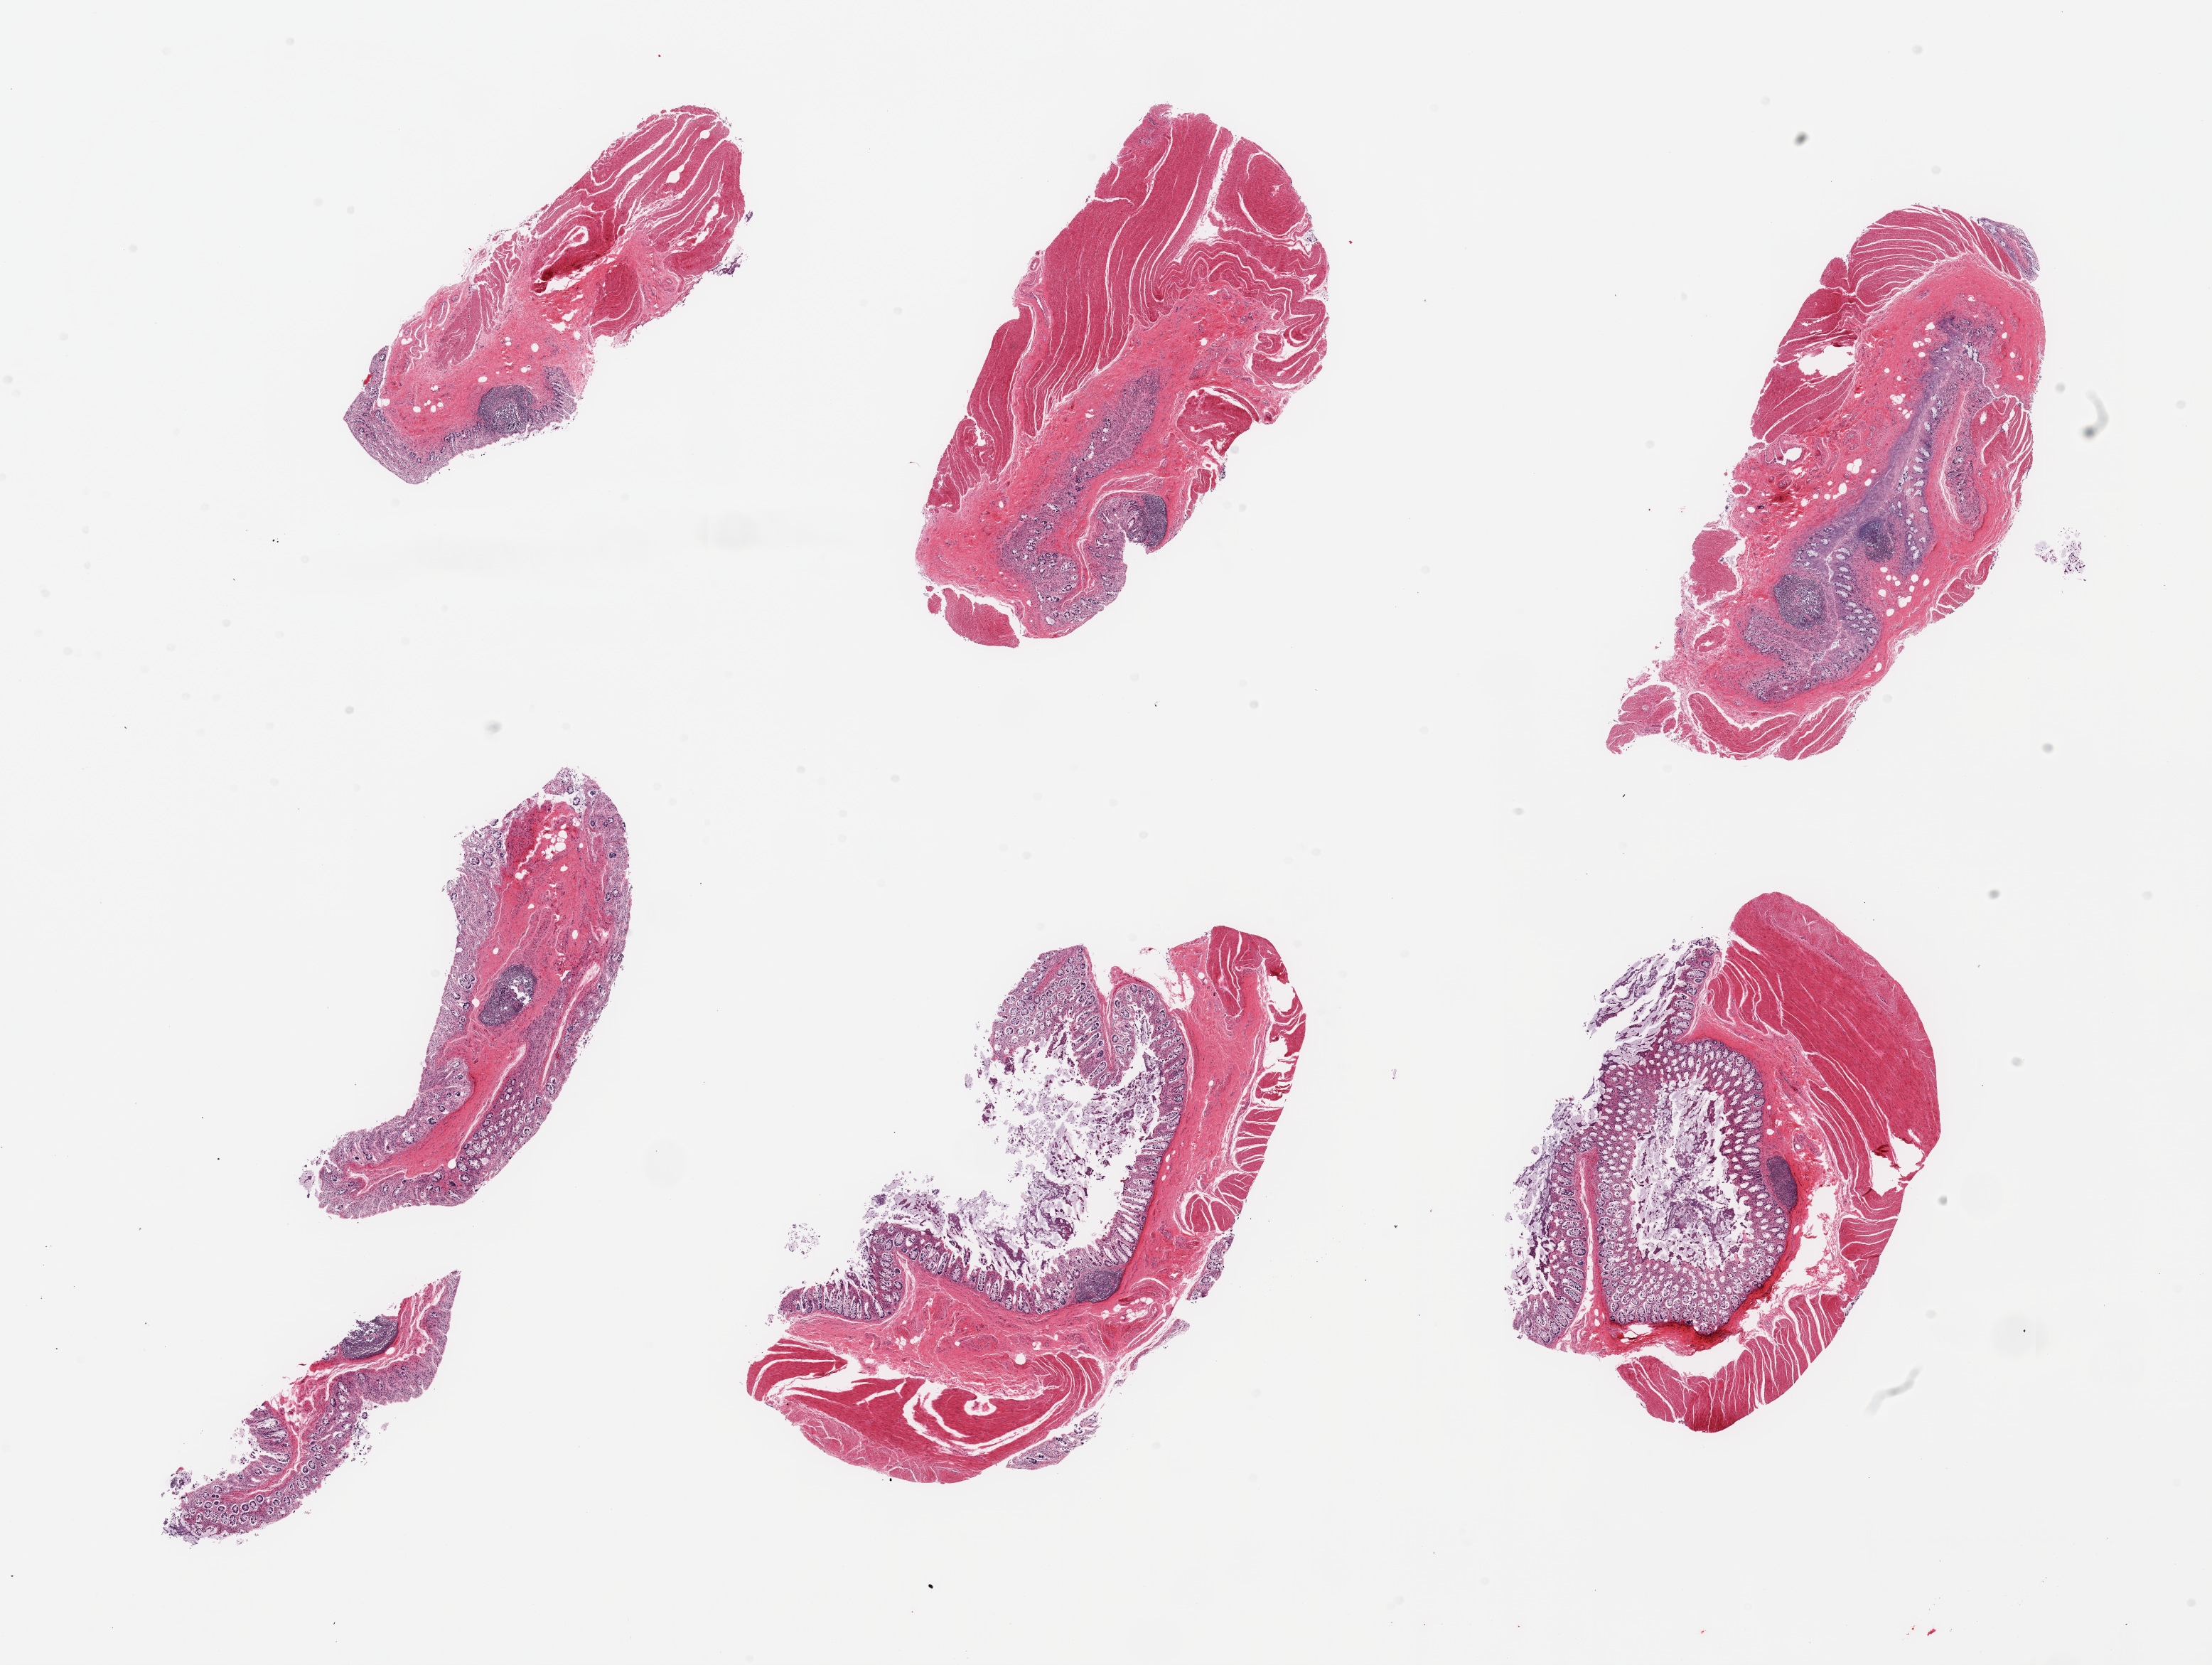
Whole-slide image, hematoxylin and eosin (H&E) stain, low-resolution overview of the scanned area, about 24.6 x 18.5 mm; PAXgene-fixed paraffin-embedded (PFPE) section; sampled site (target tissue): transverse colon; tissue donor sample. Donor: male.
• review note (as recorded): 7 pieces; most include both moderately to severely autolyzed mucosa and muscularis